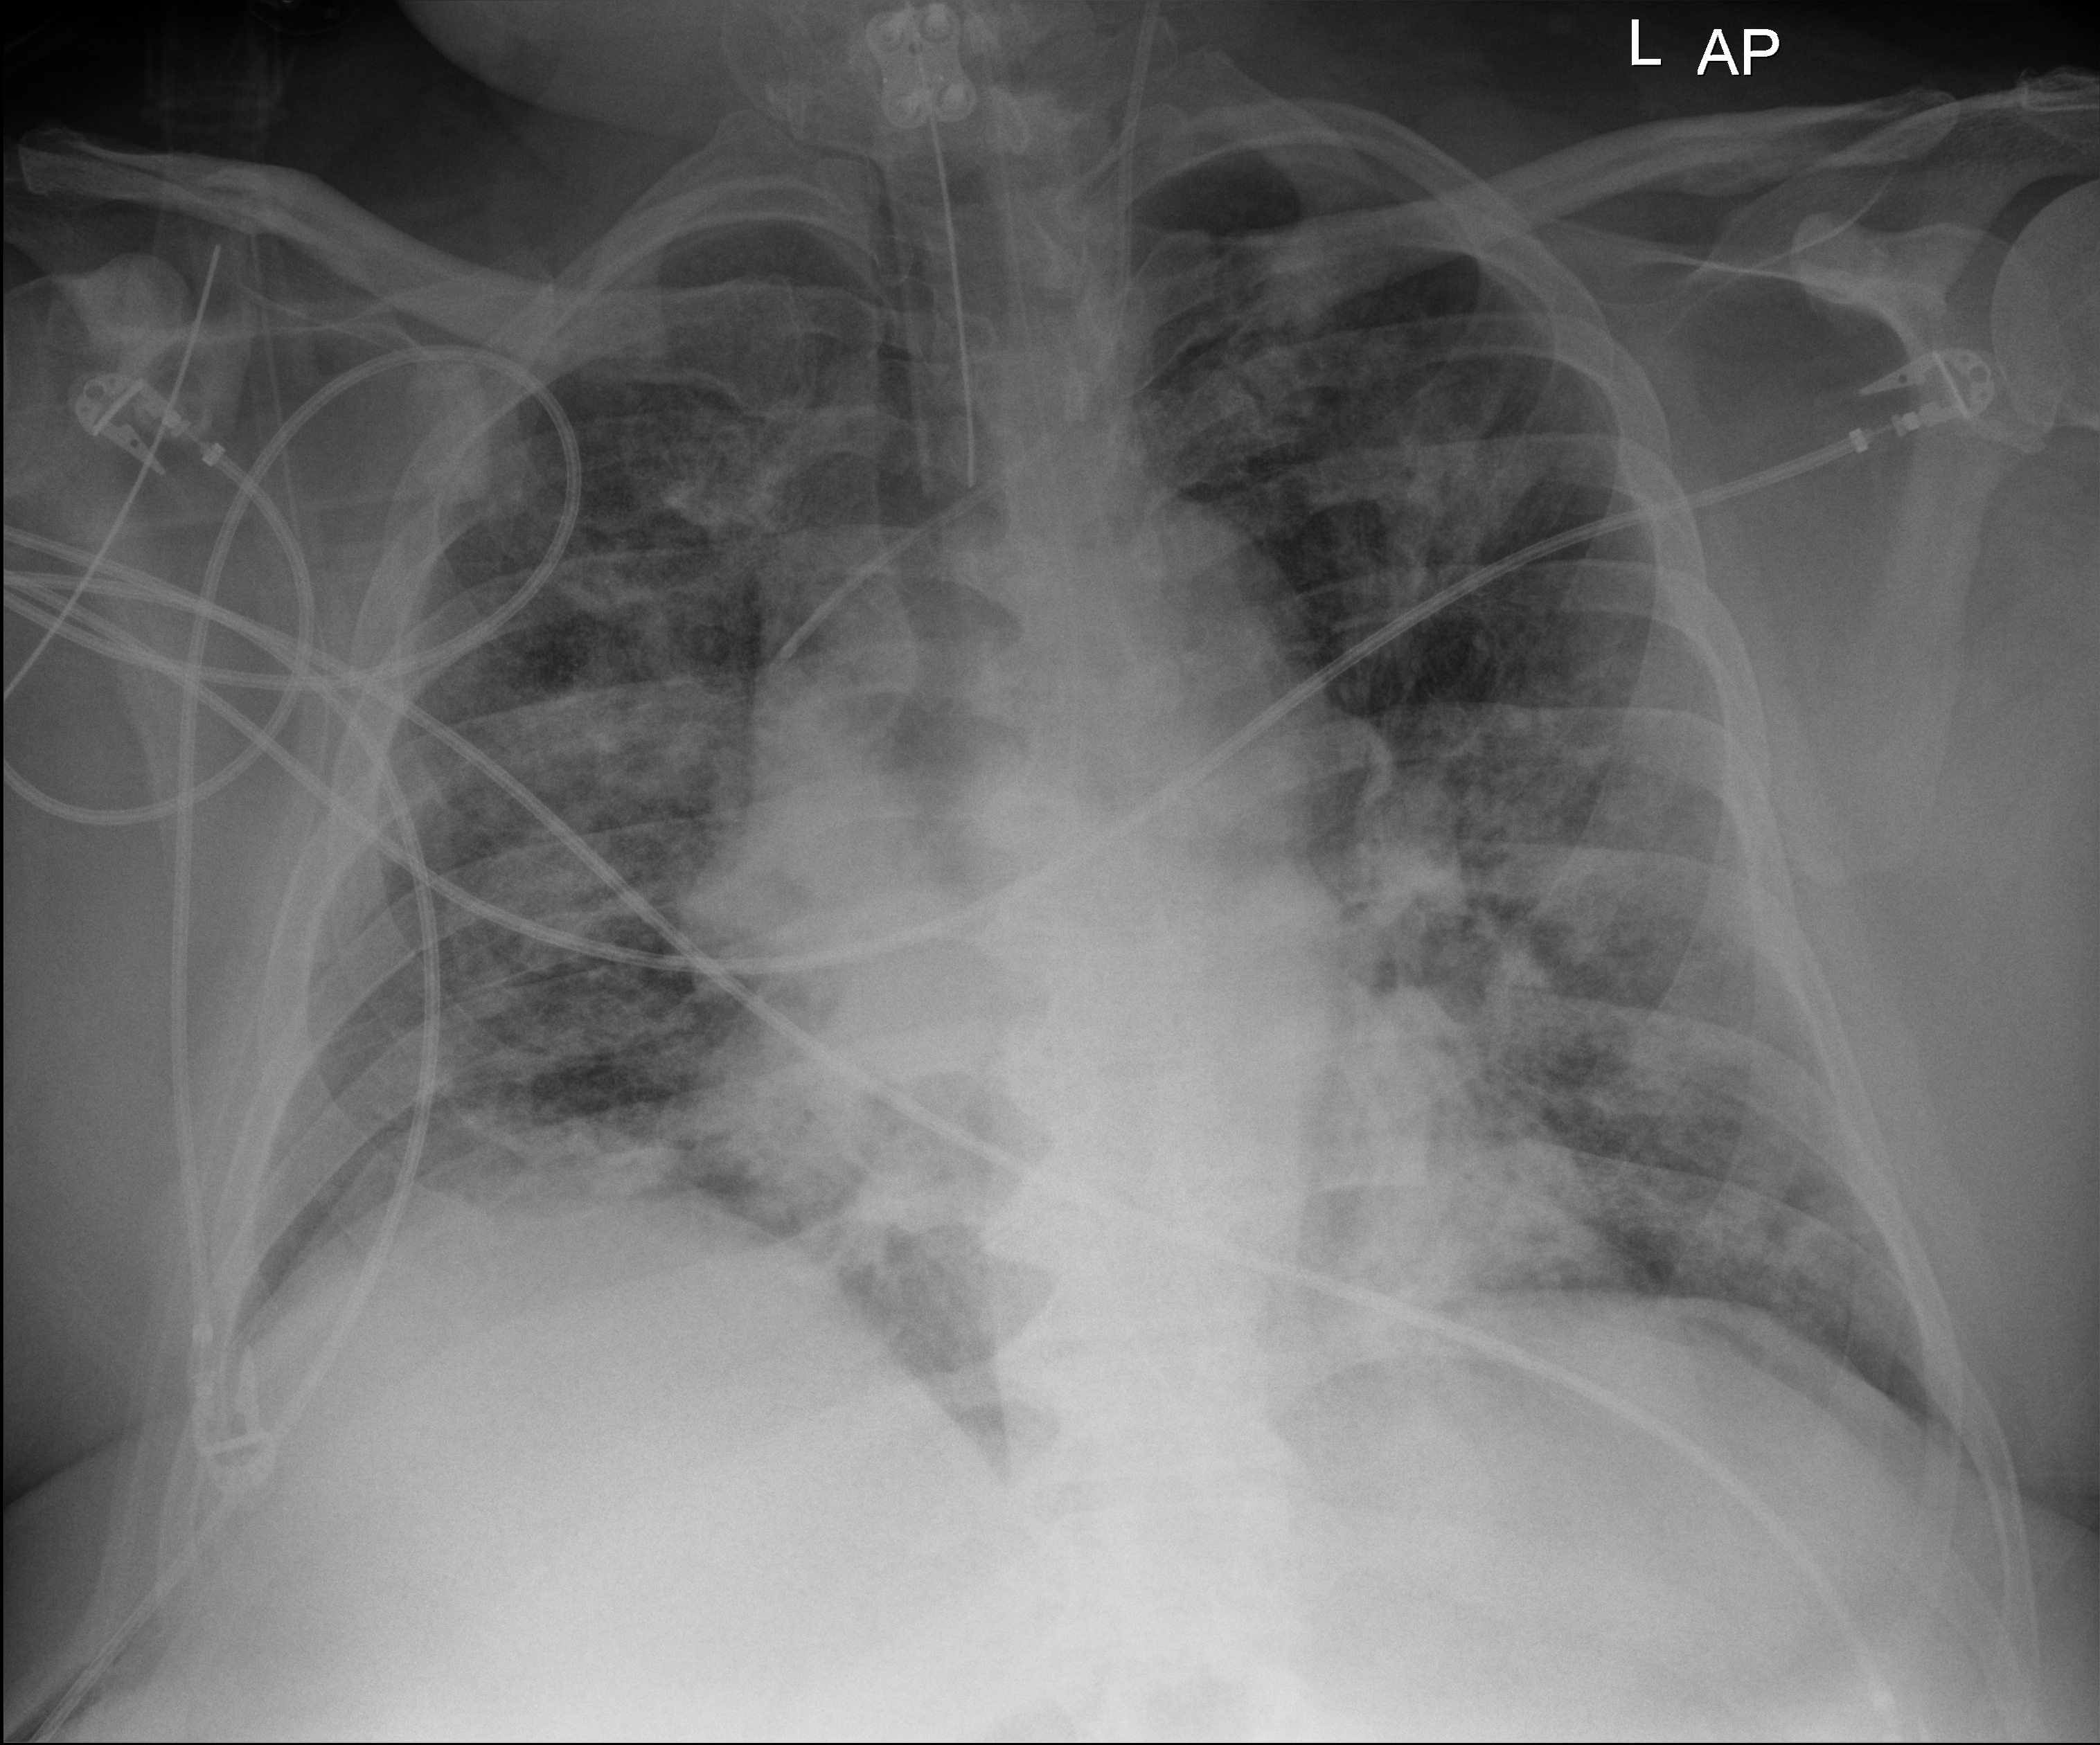
Bedside chest radiograph (digital radiography), anteroposterior (AP) projection. Patient hospitalised with COVID-19; male, aged 18–59 years.
Admission-level facts for this patient (not findings on this image; timing relative to this image not recorded): length of hospital stay: 47 days; diabetes (admission record): no.